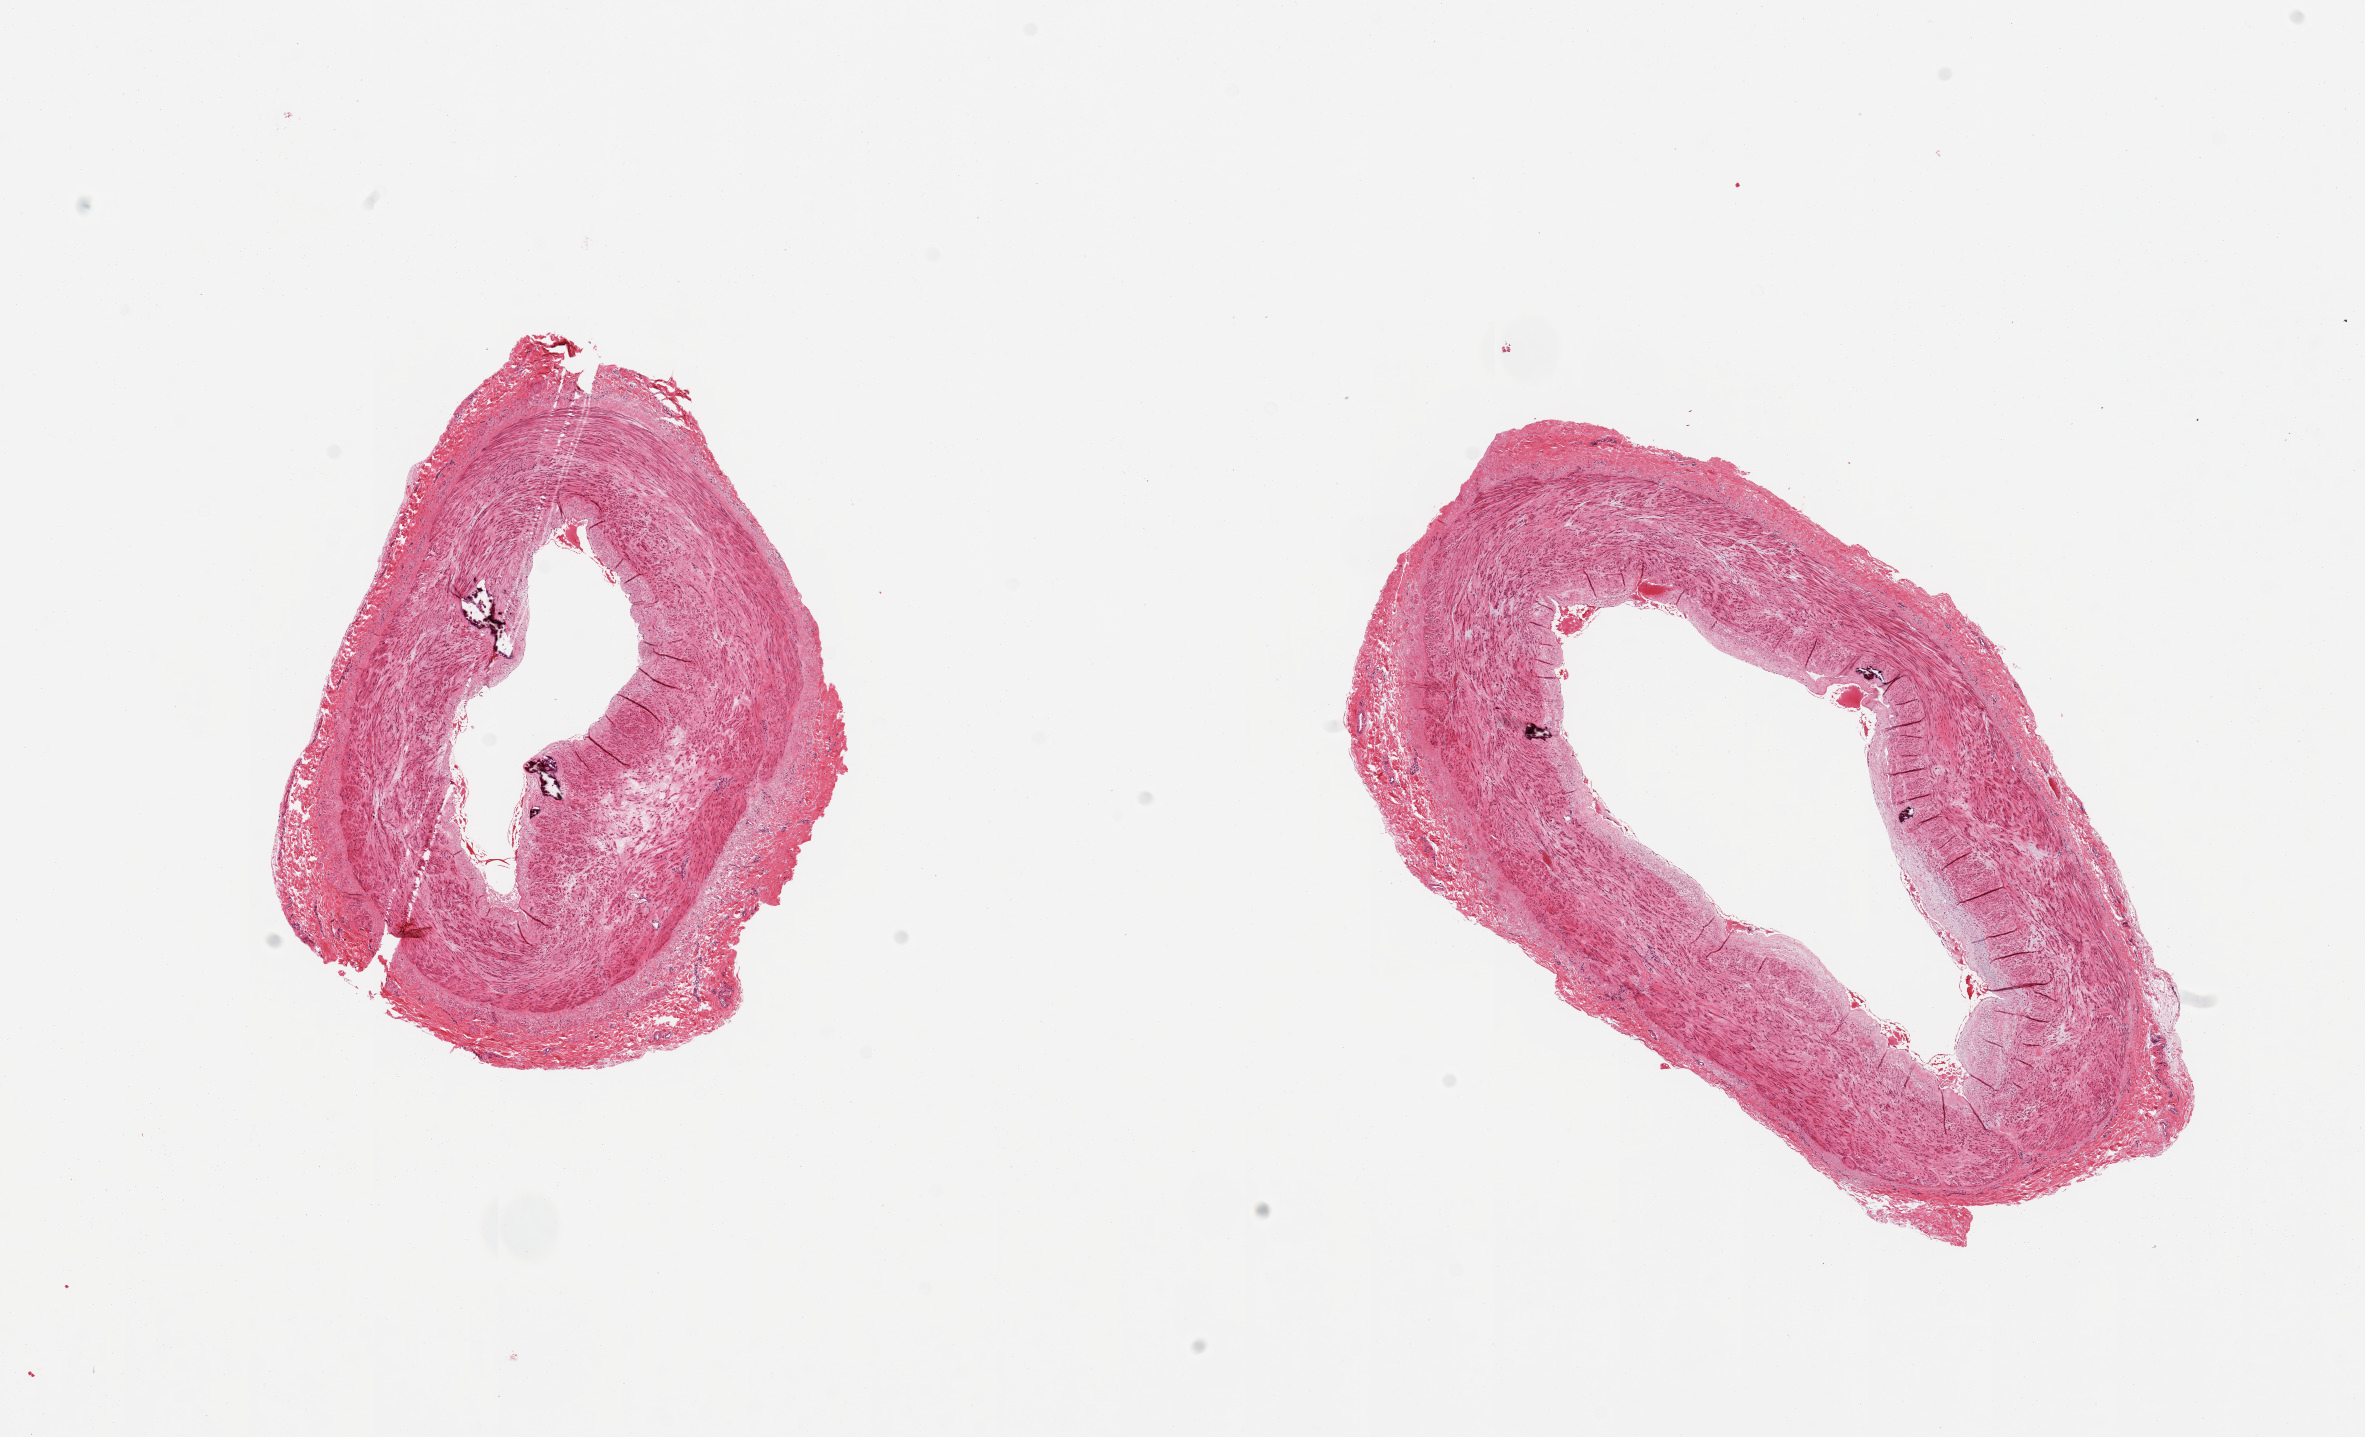
H&E whole-slide image, shown as a low-resolution overview of the whole scanned area (about 18.7 x 11.4 mm); PAXgene-fixed, paraffin-embedded tissue; section of tibial artery (target tissue); tissue donor sample. Donor sex: male.
• pathologist's review note for this sample: 2 pieces; medial calcific sclerosis, mild atherosclerosis